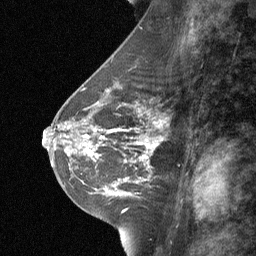
Breast MRI (dynamic contrast-enhanced), one sagittal slice. Slice 32 of 64 in the series (ordered by position). Dynamic contrast-enhanced study with each time point stored as its own series, time point 2 of 3 at this slice position (early post-contrast, ordered by acquisition time). 1.5 T. TE 4.8 ms, TR 27 ms. 2 mm slice thickness. 256 × 256 image matrix, field of view 180 × 180 mm. Female patient, age 42 years. From the clinical record (not read from this slice): setting: breast cancer imaged before/during neoadjuvant chemotherapy; receptor status: triple-negative.
Structures marked on this image (semi-automatically segmented with operator editing):
- analysis volume of interest (the breast-tissue region the enhancement analysis was run in; not a lesion): bounding box [x1, y1, x2, y2] px = [99, 117, 173, 187]
- tumour enhancement mask (voxels above the 90 % enhancement threshold inside the analysis volume of interest): [134, 120, 167, 164]